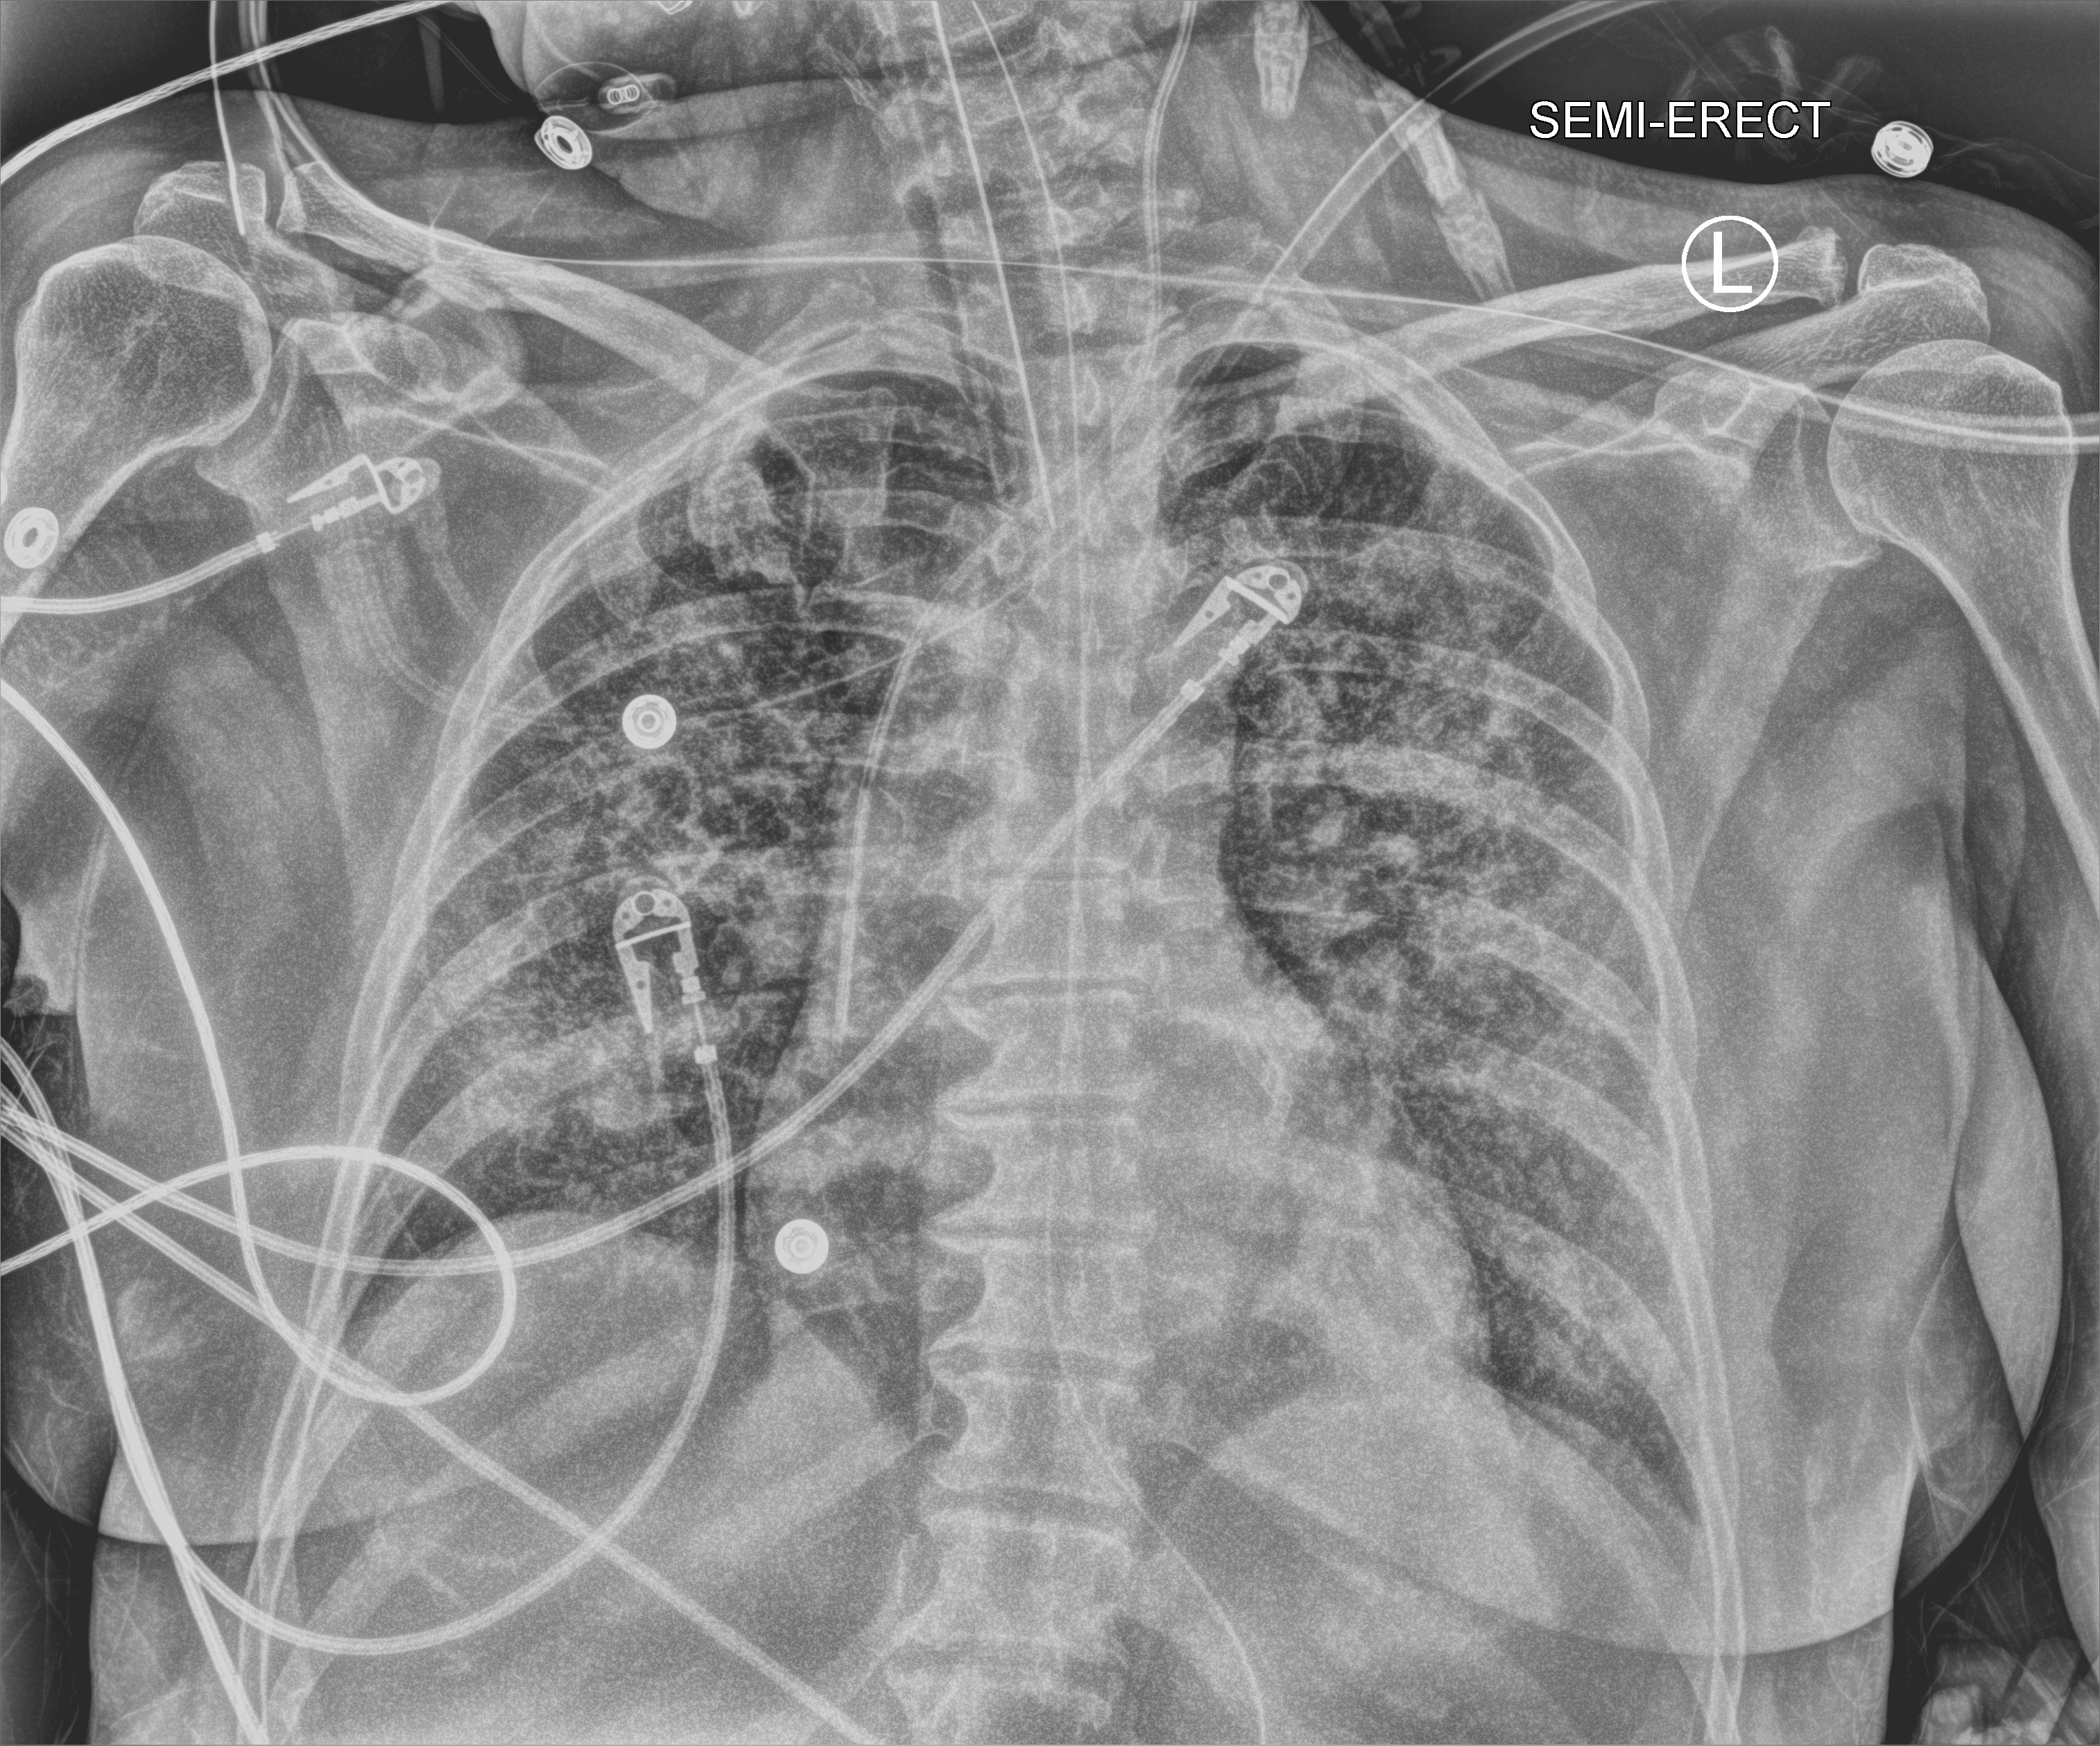
Bedside chest radiograph (computed radiography), anteroposterior (AP) projection. Female patient hospitalised with COVID-19, age 60–74 years.
Admission-level facts for this patient (not findings on this image; timing relative to this image not recorded): chronic kidney disease (admission record): no; admitted to intensive care during this hospital stay: yes.